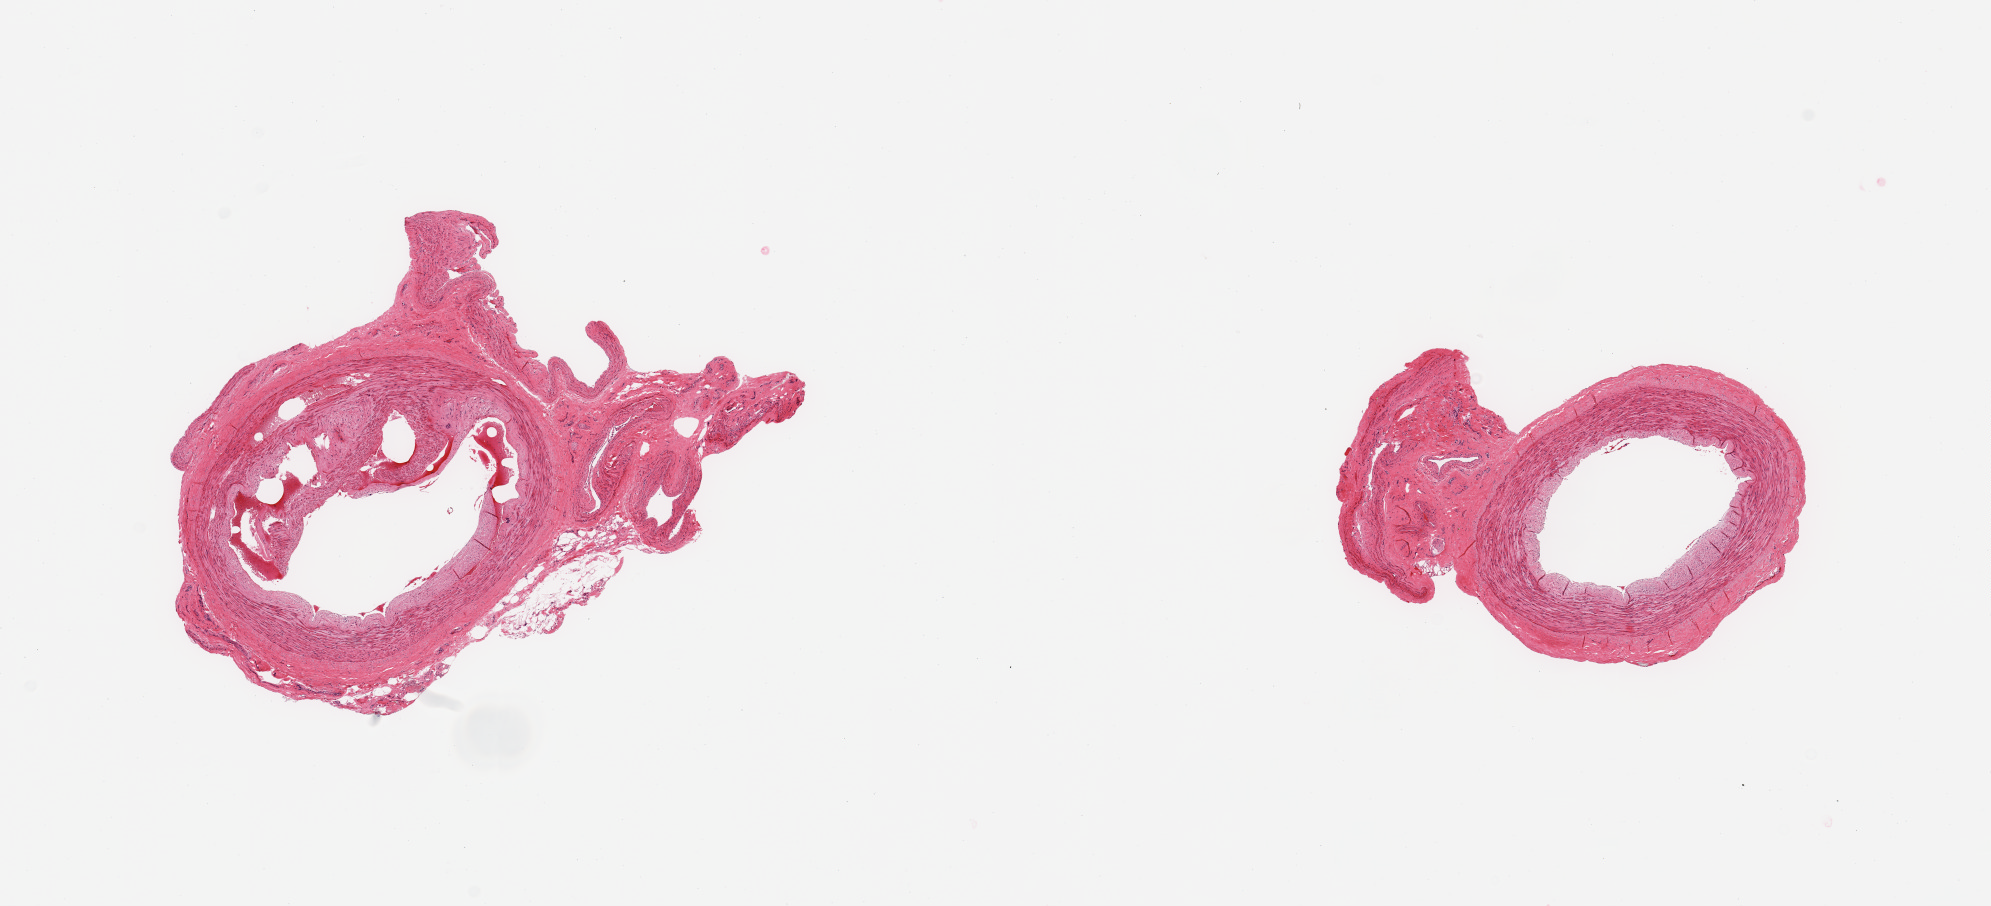
H&E whole-slide image — low-resolution overview of the scanned area, about 15.8 x 7.2 mm (from a 20x scan), PAXgene-fixed paraffin-embedded (PFPE) section, sampled site (target tissue): tibial artery, donor tissue sample. Male donor.
Review note (as recorded): 2 pieces; some sclerosis, attachment of vessels.